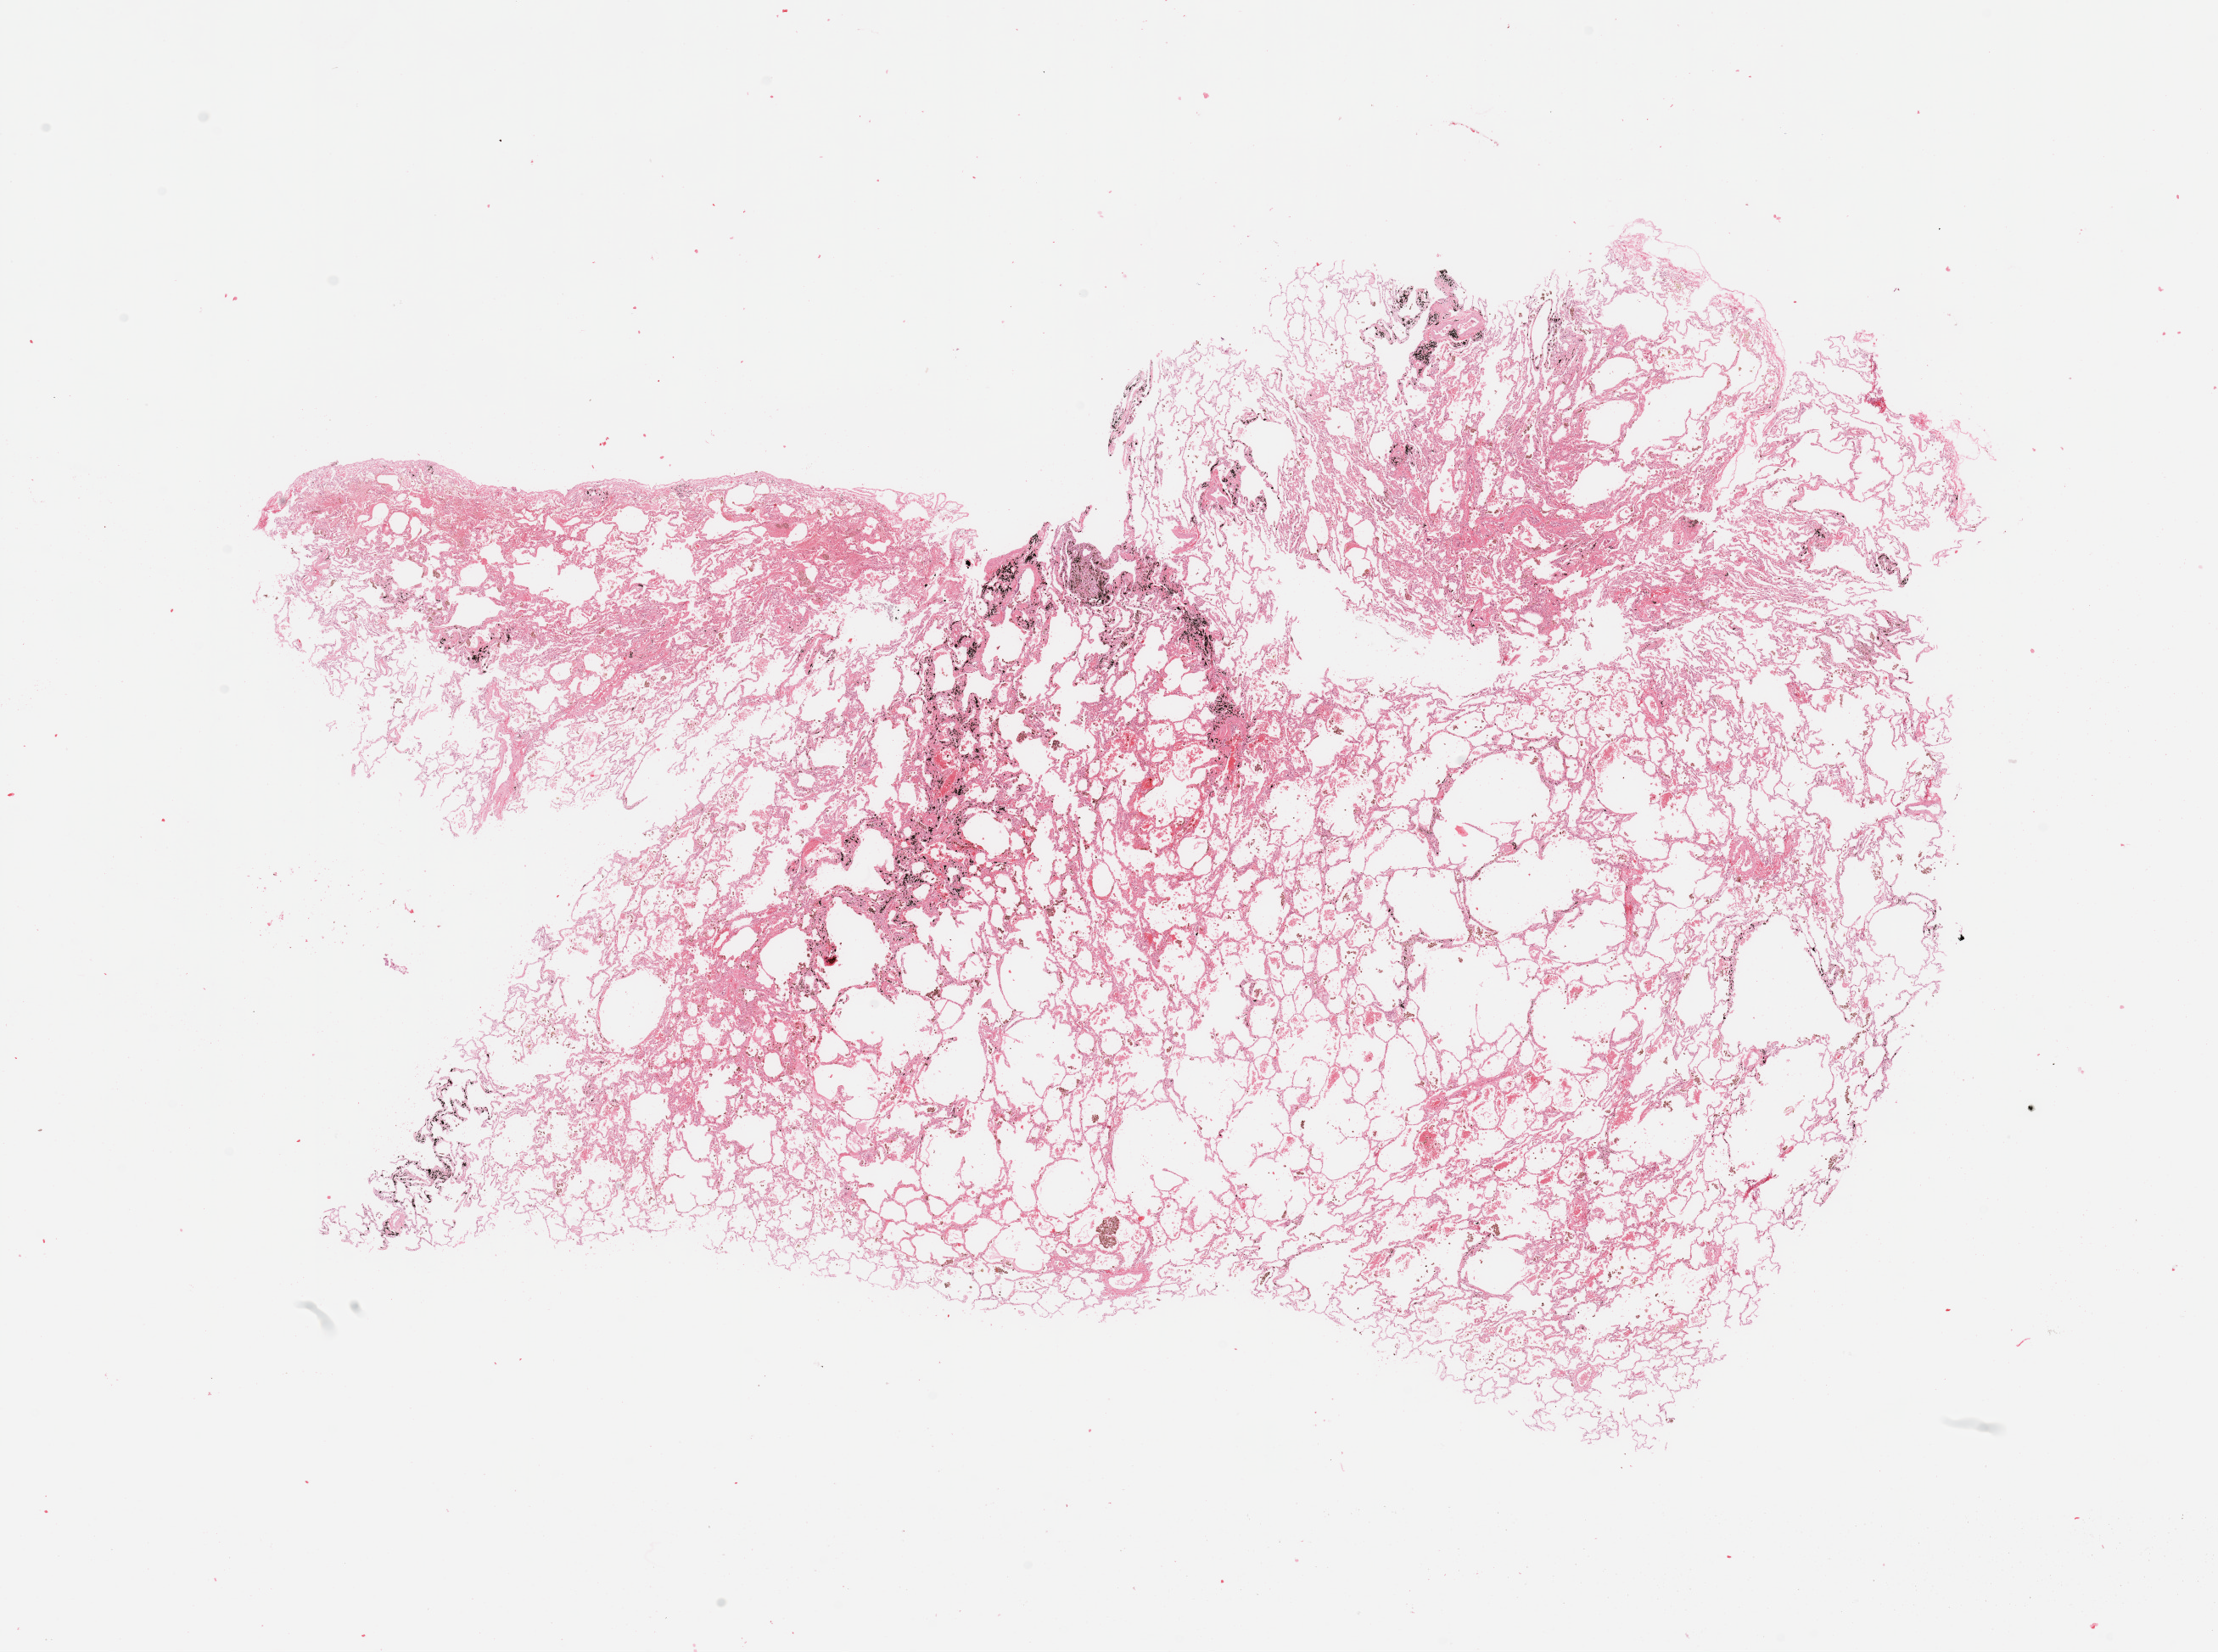
Whole-slide histology image, Hematoxylin and eosin (H&E) stained, shown as a low-resolution overview of the whole scanned area (about 20.7 x 15.4 mm), normal (non-tumour) tissue sample, sampled site: lung. Patient: male, age 48 years.
This section: normal (non-tumour) tissue from the same patient. Patient diagnosis: Adenocarcinoma, NOS.